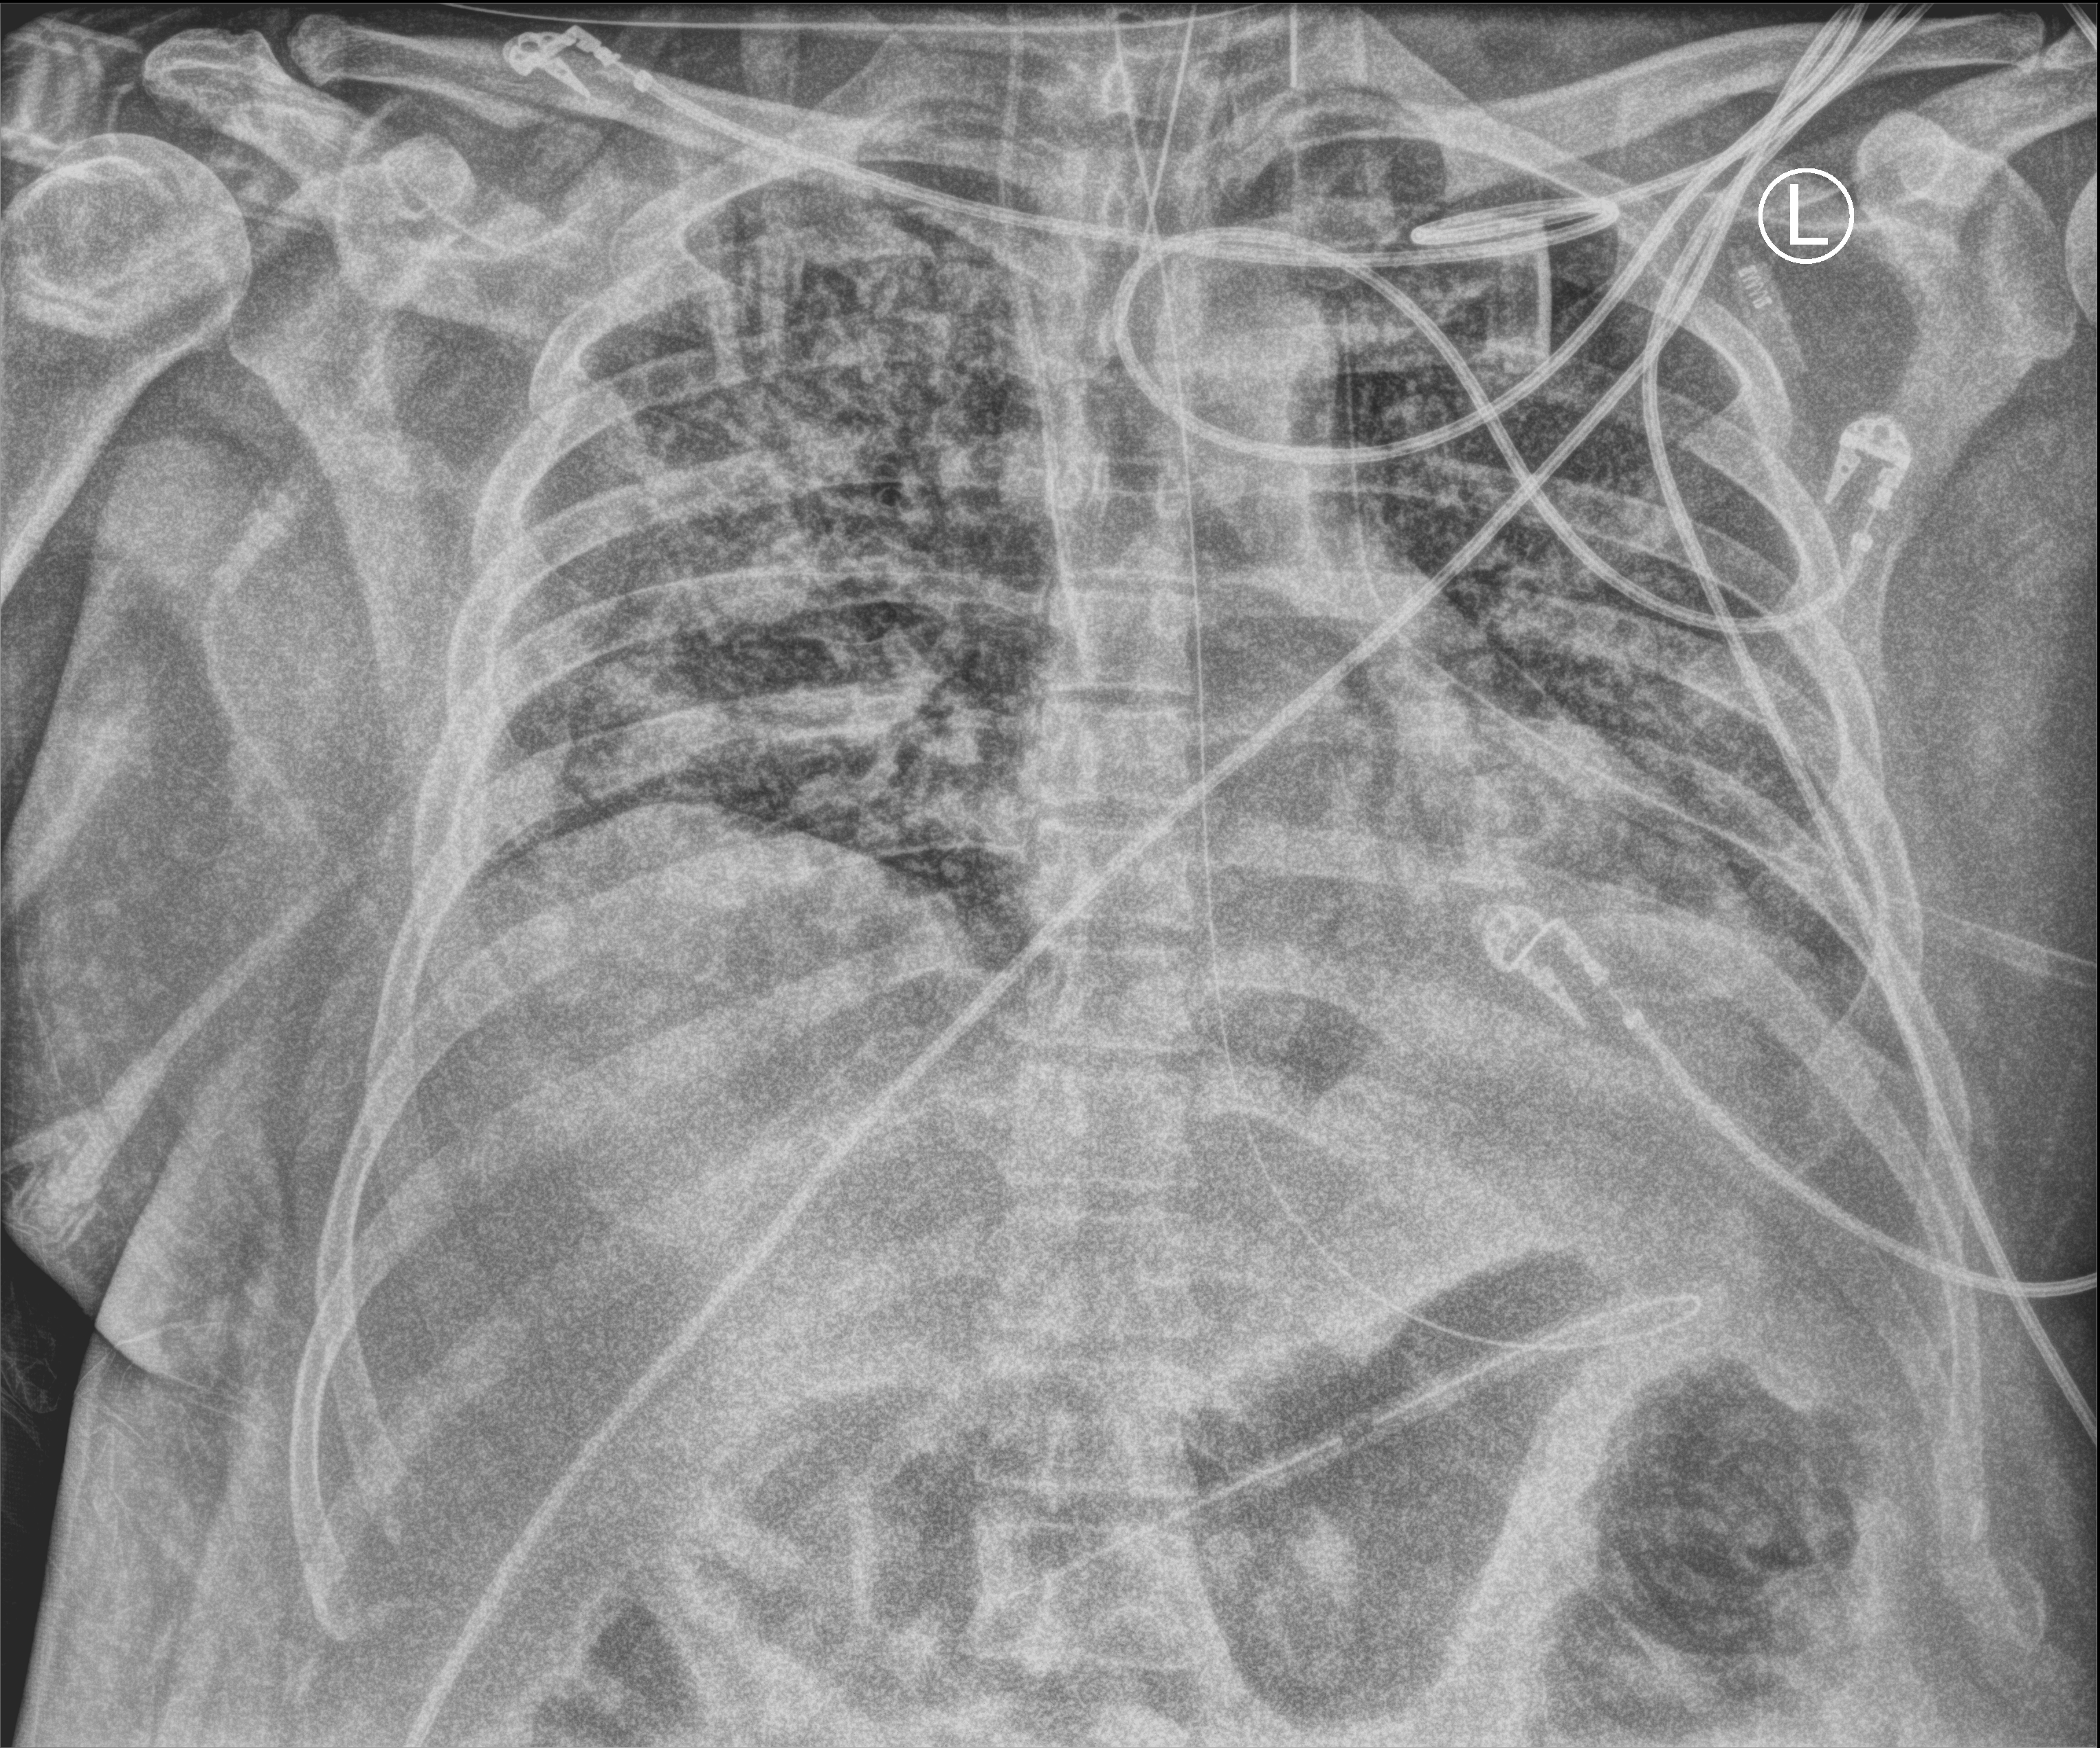
Chest X-ray (portable), anteroposterior (AP) projection. Male patient hospitalised with COVID-19, age 18–59 years.
Hospital-stay facts (about this admission, not read from this image; timing relative to this image not recorded): hypertension (admission record): no.